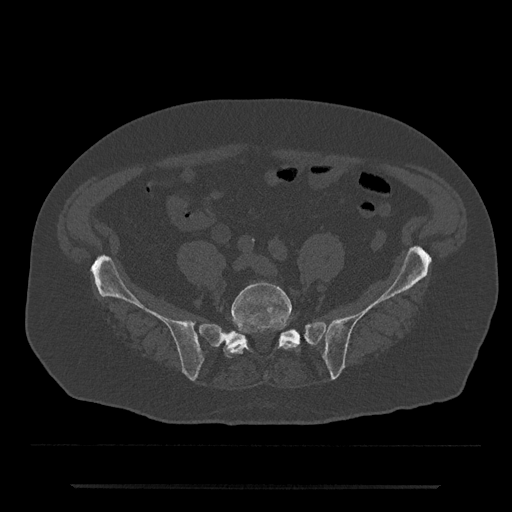
CT including the spine, one axial slice; slice 266 of 797 in the series (ordered by position); reconstruction kernel Br40s/3; 120 kVp; bone window (W 1800 / L 400 HU); 0.5 mm slice thickness; 512 × 512 image matrix, field of view 434 × 434 mm. Patient: male, 80 years. Case-level facts recorded for this patient, not image findings: primary cancer: prostate; vertebrae with lytic lesions (as recorded): L1, T11.
Outlined on this slice (semi-automatically segmented with operator editing):
- L5 vertebra: bounding box <223,282,297,357> (left, top, right, bottom; pixels)